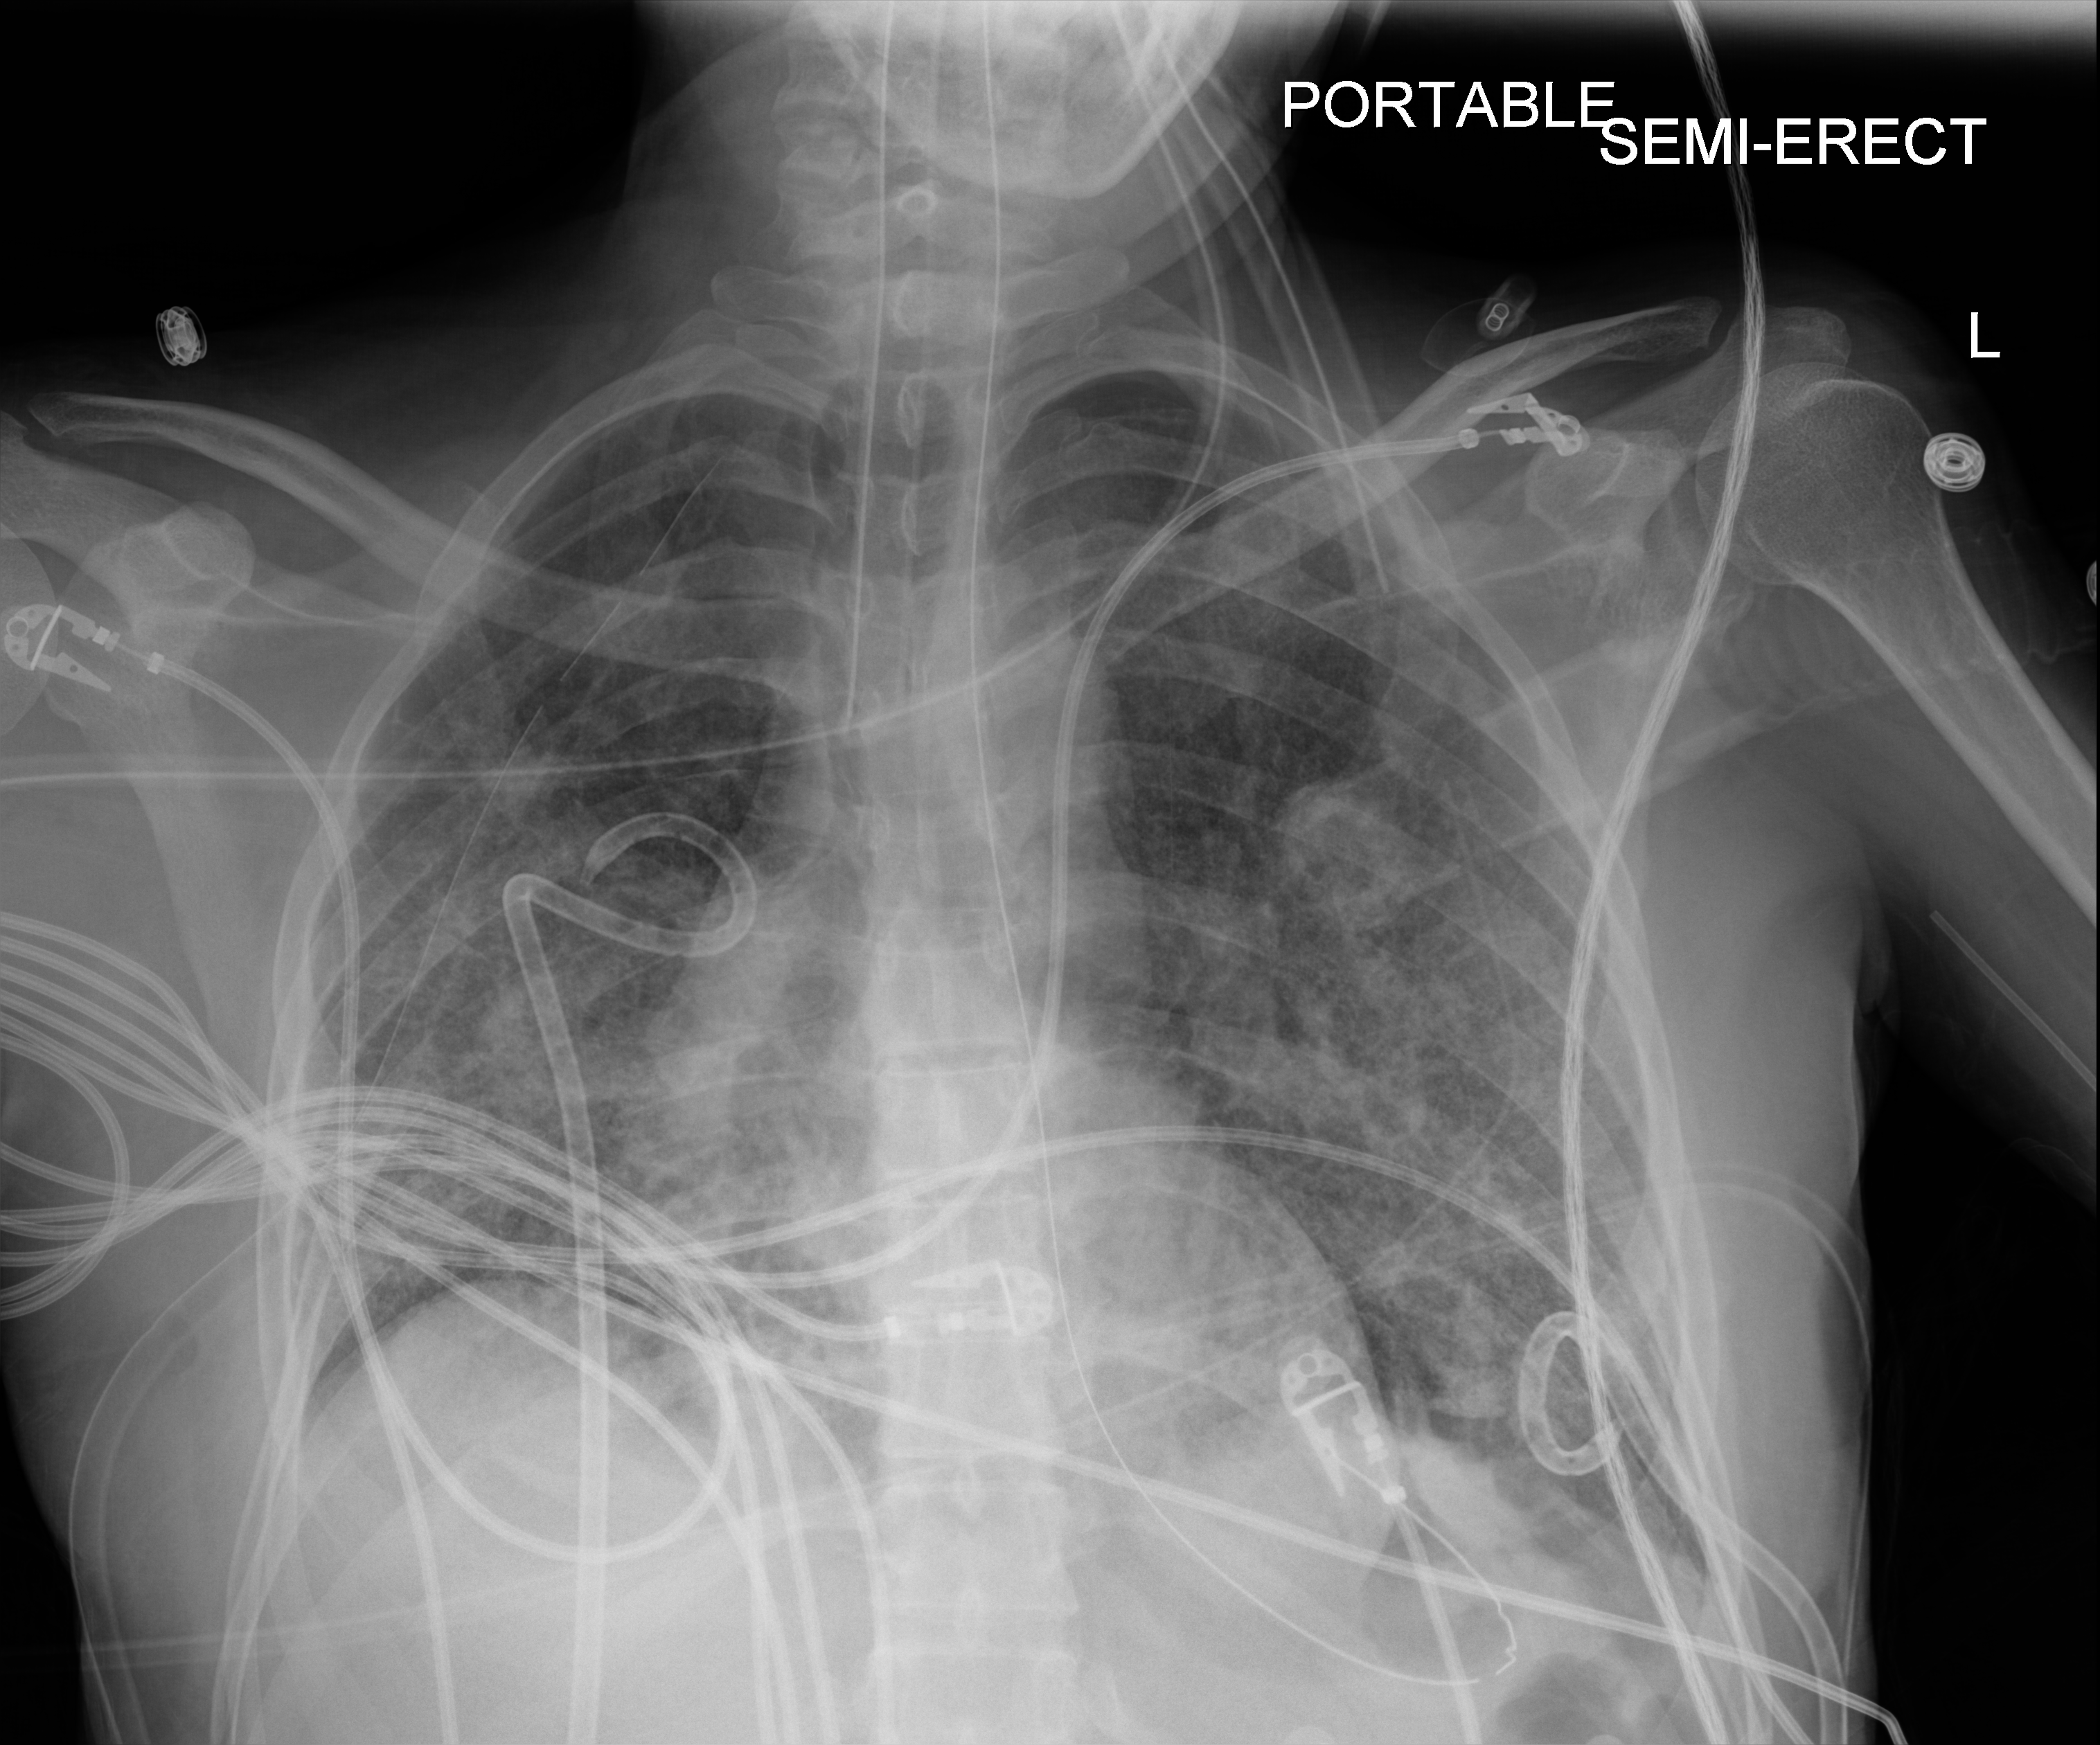
Chest radiograph (digital radiography); anteroposterior (AP) projection. Patient hospitalised with COVID-19, aged 18–59 years.
Hospital-stay facts (about this admission, not read from this image; timing relative to this image not recorded):
- length of hospital stay: 41 days
- admitted to intensive care during this hospital stay: yes
- mechanically ventilated during this hospital stay: yes